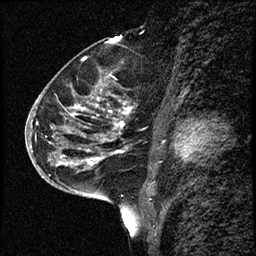
Breast MRI (dynamic contrast-enhanced), one sagittal slice. Position 35 of 68 along the scan axis. Dynamic contrast-enhanced study with each time point stored as its own series, time point 2 of 3 at this slice position (early post-contrast, ordered by acquisition time). 1.5 T. TE 4.2 ms, TR 17.6 ms. 2 mm slice thickness. 256 × 256 image matrix, field of view 200 × 200 mm. Patient: female, 52 years. From the clinical record (not read from this slice): setting: breast cancer imaged before/during neoadjuvant chemotherapy; receptor status: HER2-positive.
Annotated regions visible in this slice (semi-automatically segmented with operator editing):
- analysis volume of interest (the breast-tissue region the enhancement analysis was run in; not a lesion): bounding box (x1, y1, x2, y2) in pixels: (50, 61, 147, 184)
- tumour enhancement mask (voxels above the 100 % enhancement threshold inside the analysis volume of interest): (66, 105, 129, 164)